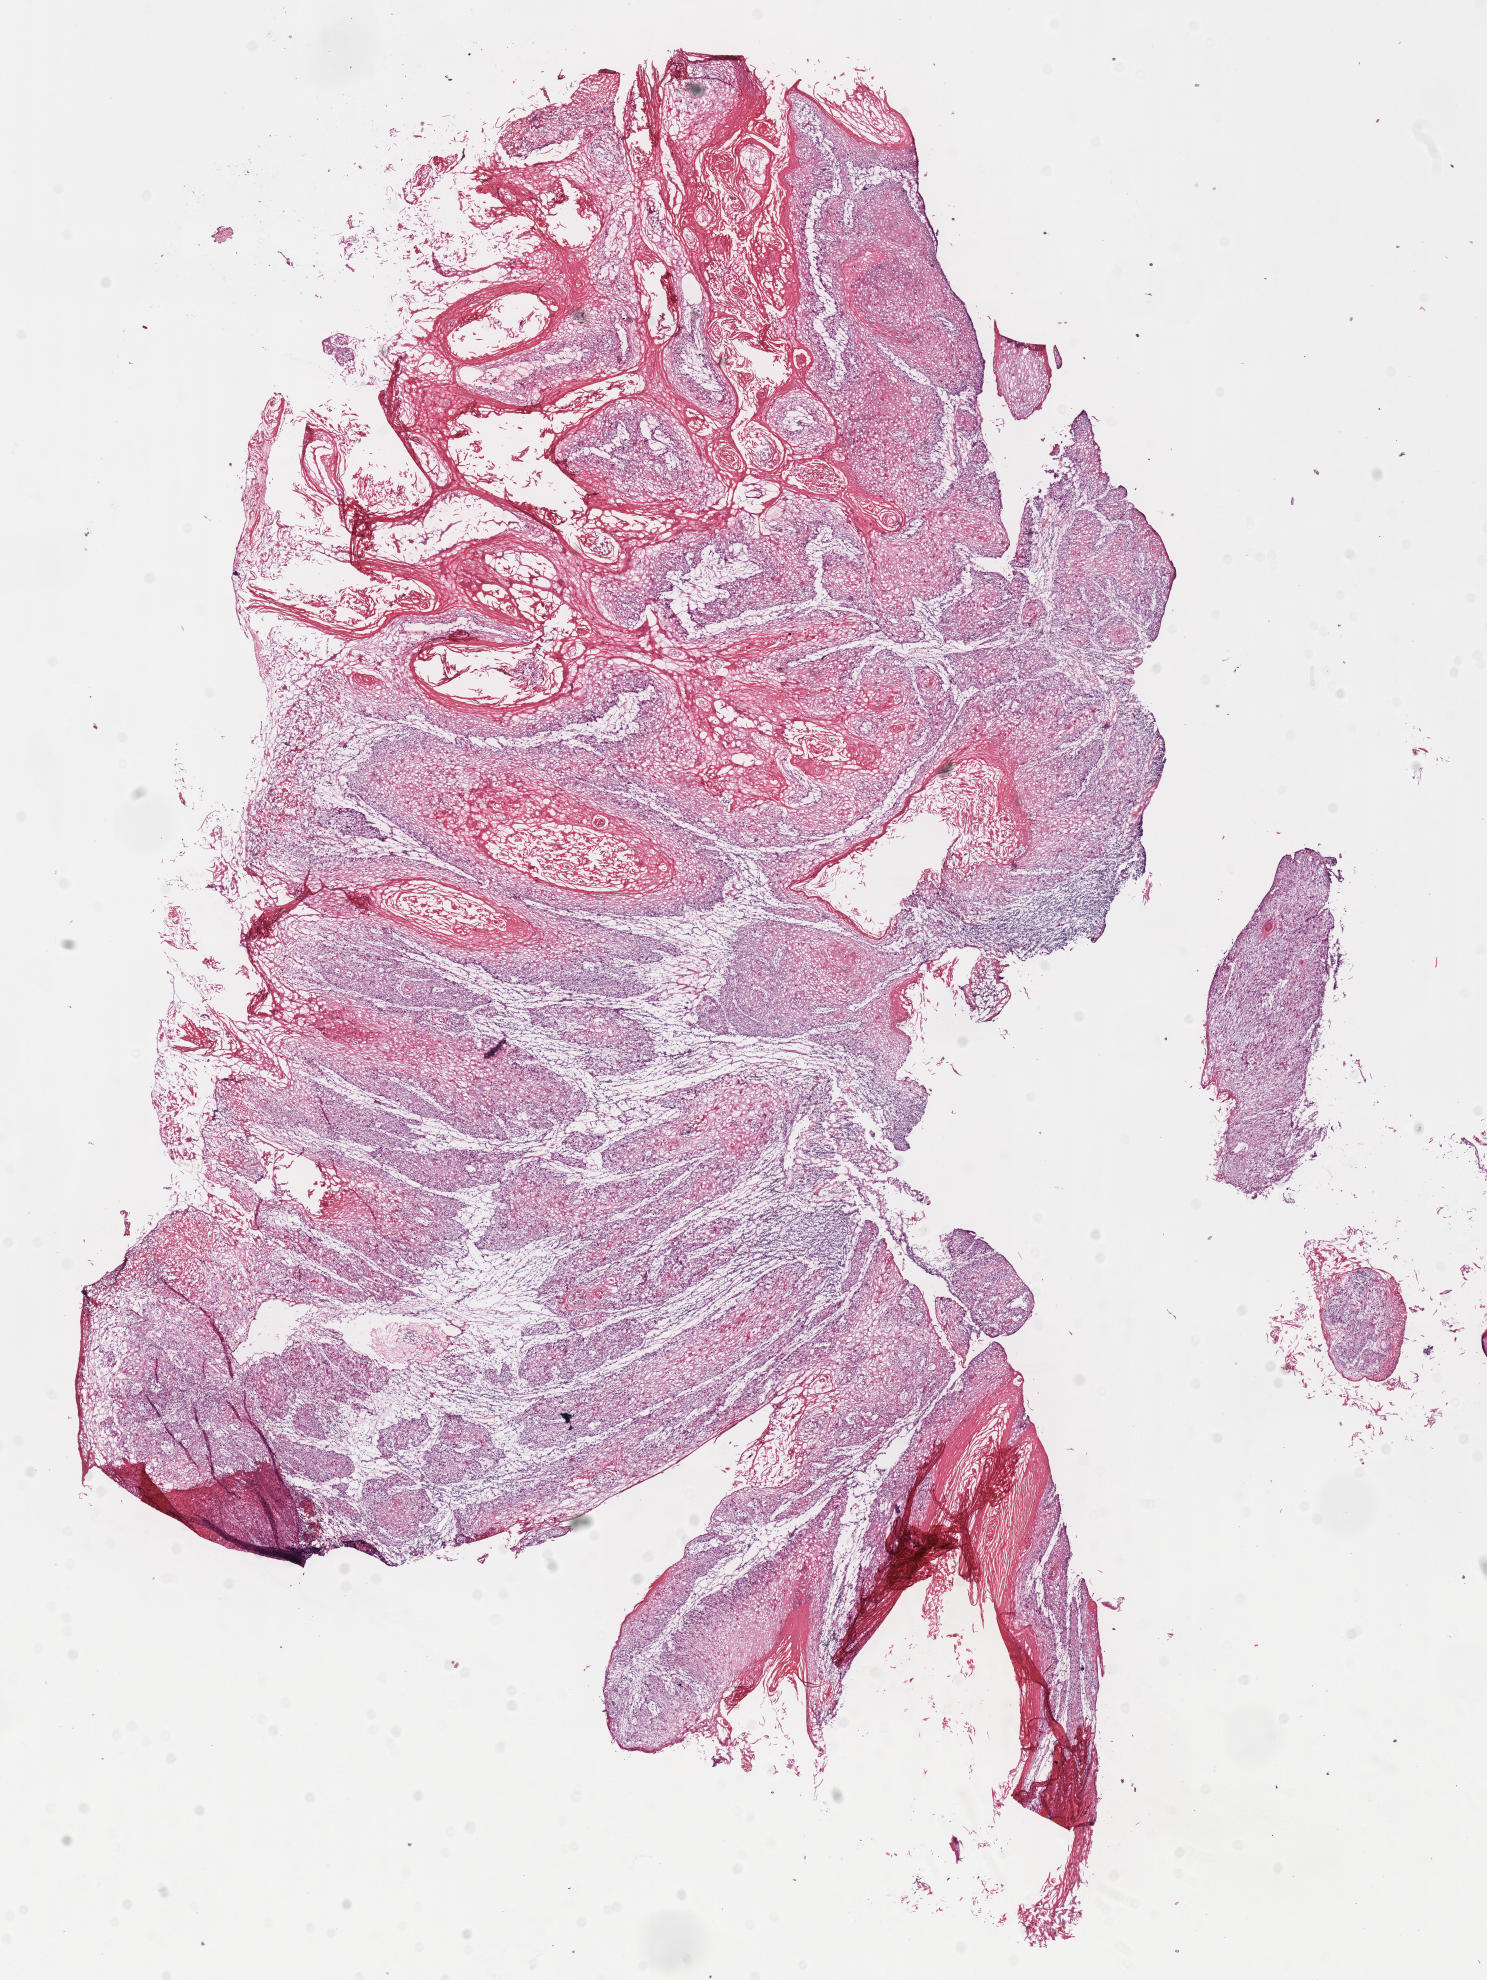
Hematoxylin and eosin (H&E) stained whole-slide image — shown as a low-resolution overview of the whole scanned area (about 11.7 x 15.6 mm). Frozen section from the top of the tissue portion. Sample: primary tumour, head and neck. Female, age 68 years at initial diagnosis. Pathologist review of this section (percent, as recorded): tumour cells 80%, tumour nuclei 80%.
Pathologic diagnosis: Squamous cell carcinoma, NOS (overlapping lesion of lip, oral cavity and pharynx).